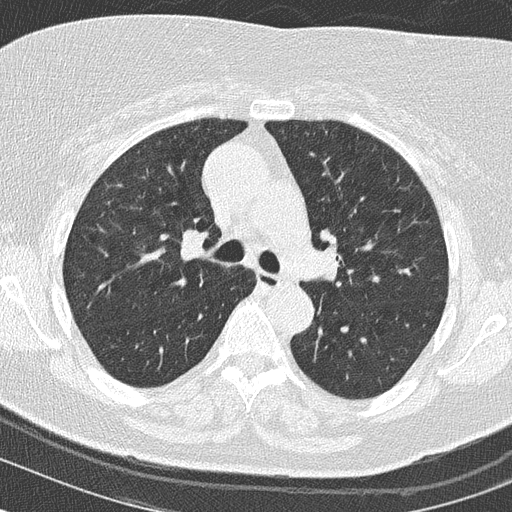
Low-dose screening chest CT, axial slice; baseline screening round; lung window (W 1500 / L -600 HU); lung (sharp) reconstruction kernel (B50f); 120 kVp; slice 48 of 149 in the series. Female, age 63 years at enrolment. Former smoker at enrolment.
- Expert-annotated lung lesion, bounding box <163,218,227,272> (left, top, right, bottom; pixels).
- Screening reader's record for this exam: no non-calcified nodule ≥4 mm recorded.
- Official screen result: negative screen, minor abnormalities not suspicious for lung cancer.